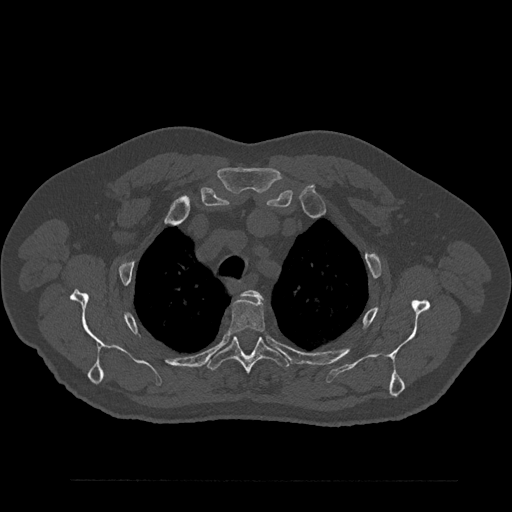
CT including the spine, one axial slice; position 665 of 797 along the scan axis; 120 kVp; bone window (W 1800 / L 400 HU); 0.5 mm slice thickness; 512 × 512 image matrix, field of view 430 × 430 mm. Male patient, age 61 years. Case-level facts recorded for this patient, not image findings: primary cancer: prostate.
Structures marked on this image (semi-automatically segmented with operator editing):
- T2 vertebra: box from (x=242, y=290) to (x=262, y=299) px
- T3 vertebra: (x=228, y=298)–(x=266, y=335)
- T4 vertebra: (x=207, y=336)–(x=289, y=375)